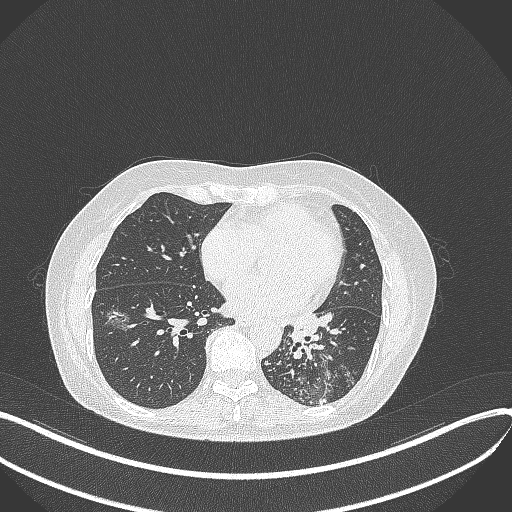
Chest CT, one axial slice. Reconstruction kernel B70f. Lung window (W 1500 / L -600 HU). 1 mm slice thickness. 512 × 512 image matrix. Female patient, age 63 years. From the clinical record (not read from this slice): clinical TNM (as recorded): T1b N0 M0; histopathological grade: G2-3.
Annotated regions visible in this slice (bounding box drawn by a radiologist):
- lung tumour (recorded histology: adenocarcinoma): box from (x=279, y=307) to (x=331, y=359) px